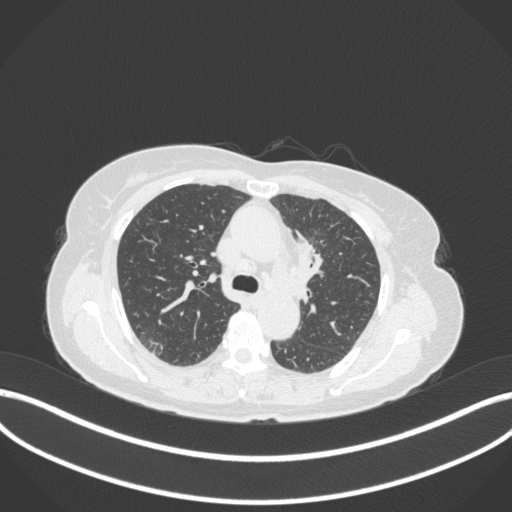
Chest CT, one axial slice; slice 225 of 368 in the series (ordered by position); reconstruction kernel B31f; lung window (W 1500 / L -600 HU); 1 mm slice thickness; 512 × 512 image matrix, field of view 400 × 400 mm. Female patient, age 65 years. From the clinical record (not read from this slice): clinical TNM (as recorded): T2a N0 M0.
Structures marked on this image (rectangle marked by the reading radiologist):
- lung tumour (recorded histology: adenocarcinoma): bounding box [x1, y1, x2, y2] px = [294, 227, 325, 281]